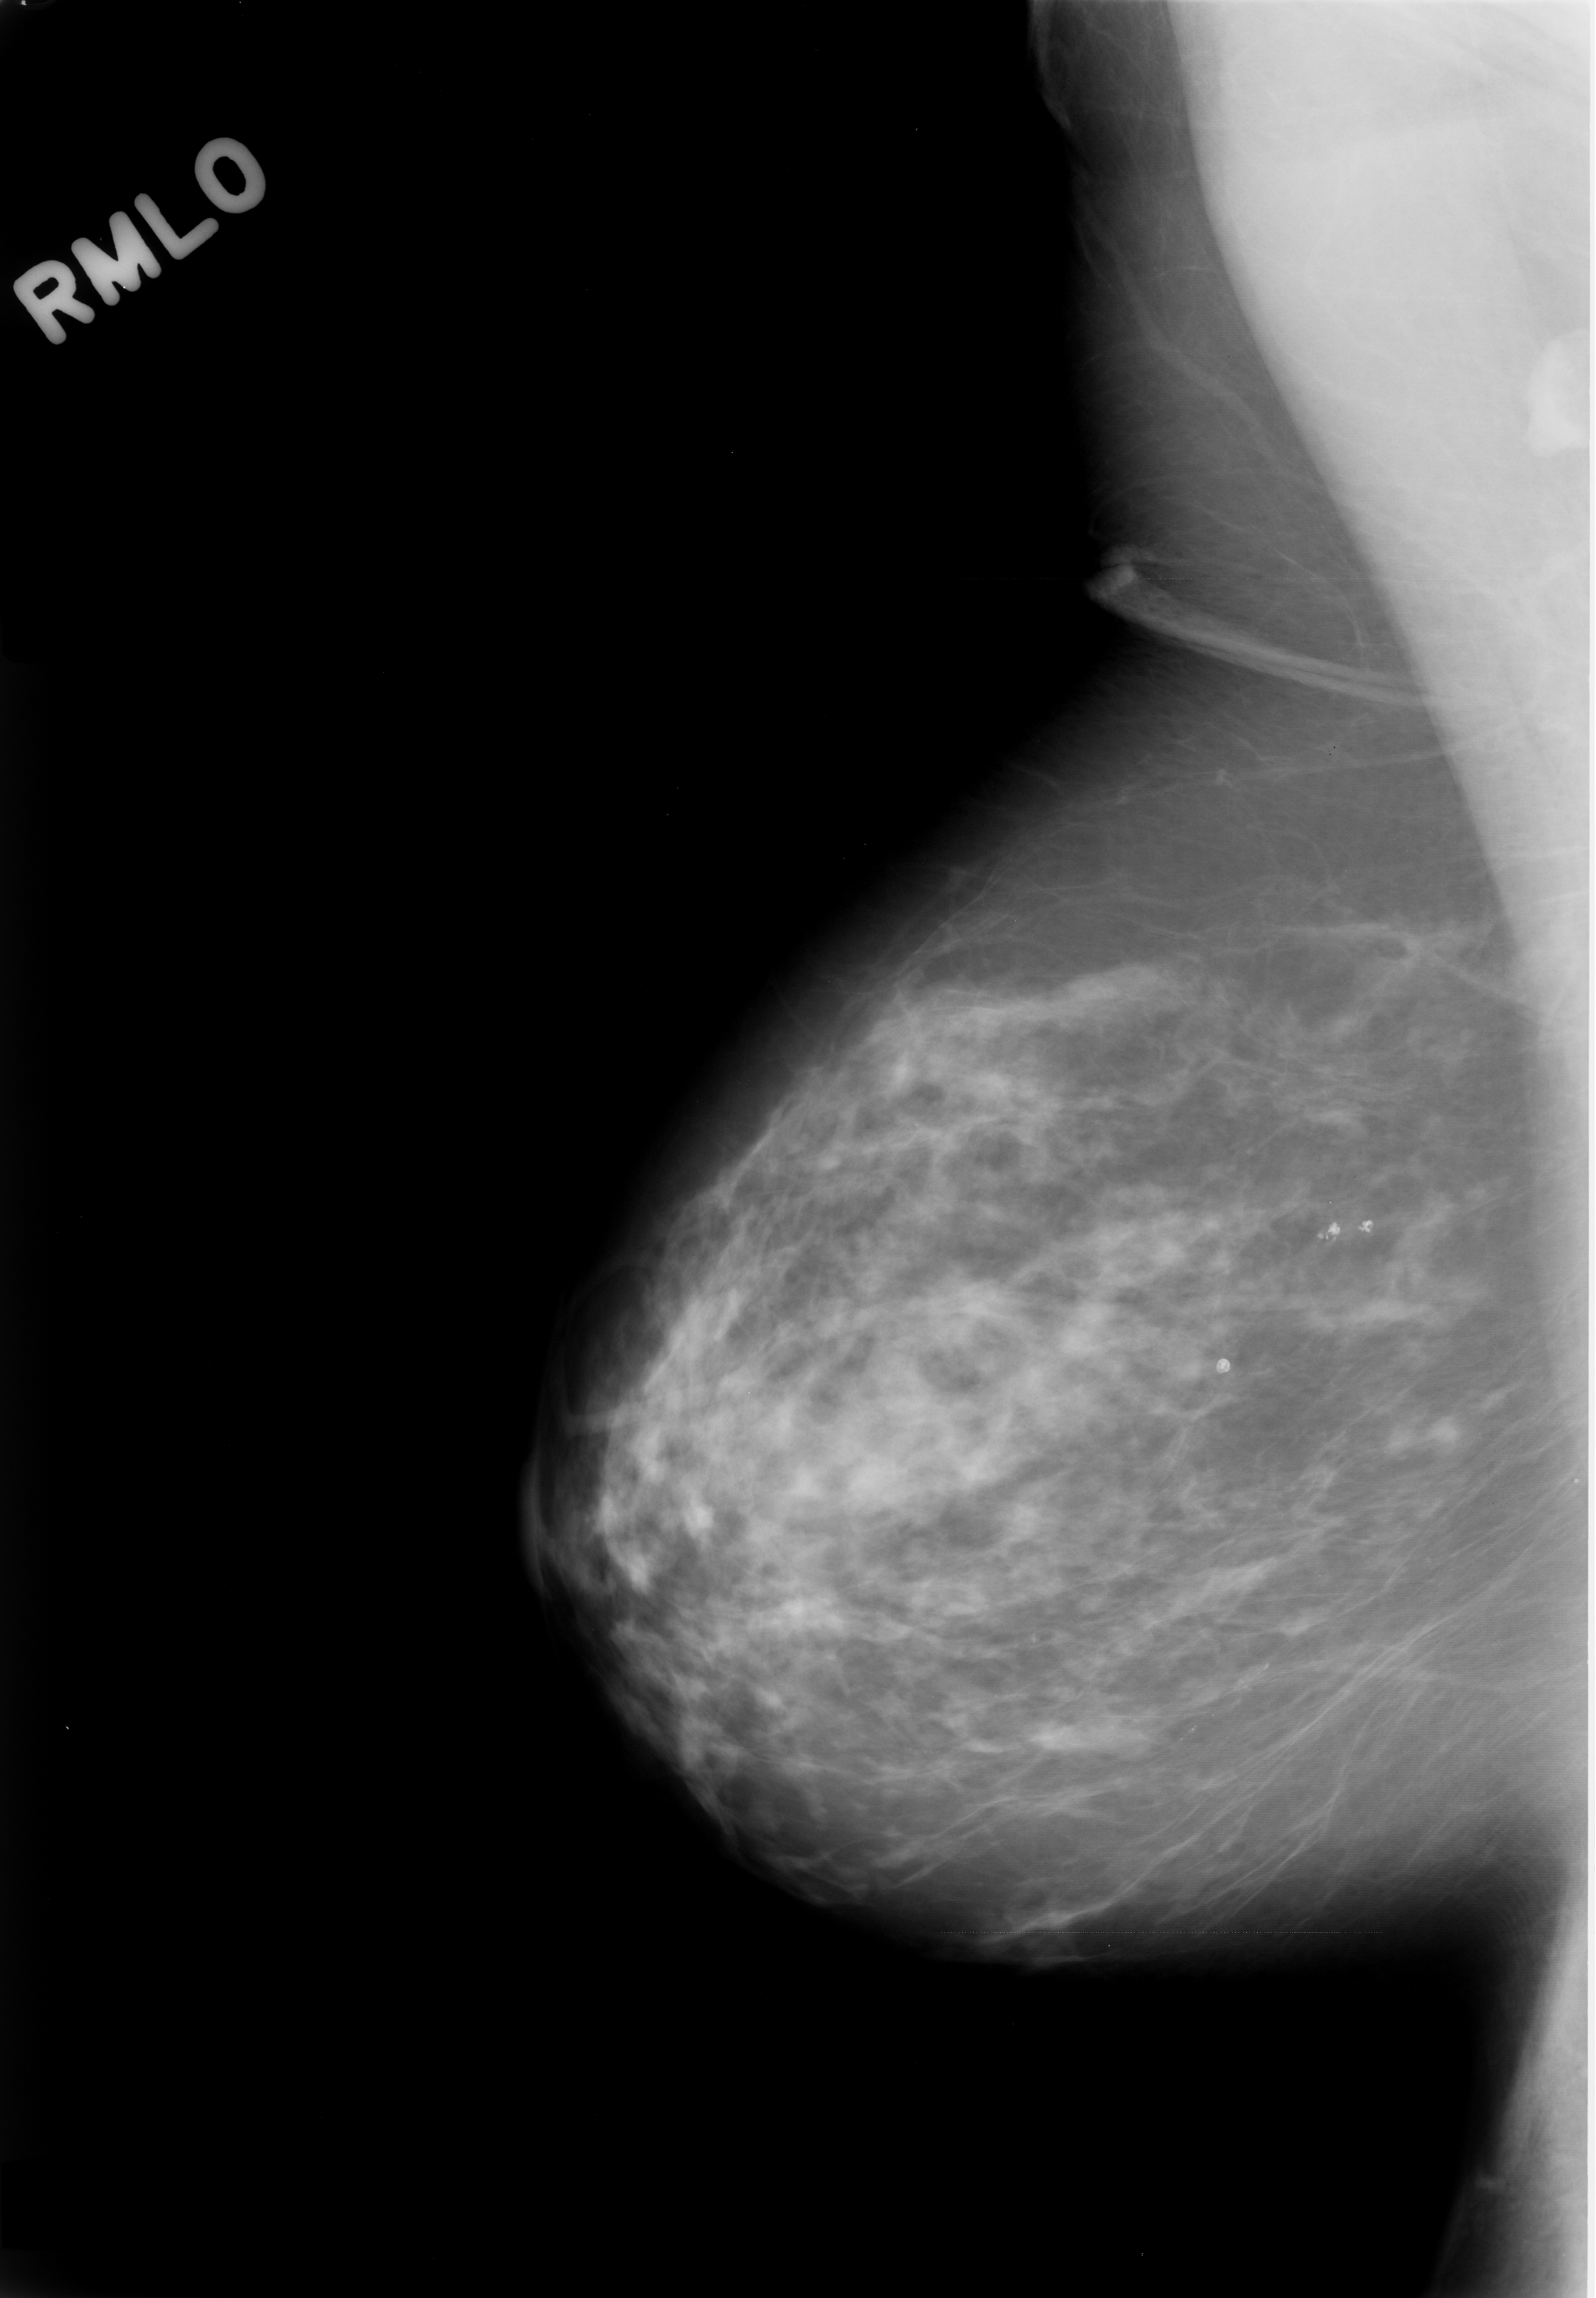
Scanned film-screen mammogram, right breast, MLO view, breast composition: scattered fibroglandular densities (BI-RADS density category 2 of 4).
Marked abnormality: calcifications, morphology fine linear branching, distribution linear; BI-RADS assessment category 4; subtlety rating 3 on a 1 (subtle) to 5 (obvious) scale; pathology result (as recorded, not read from the image): benign.